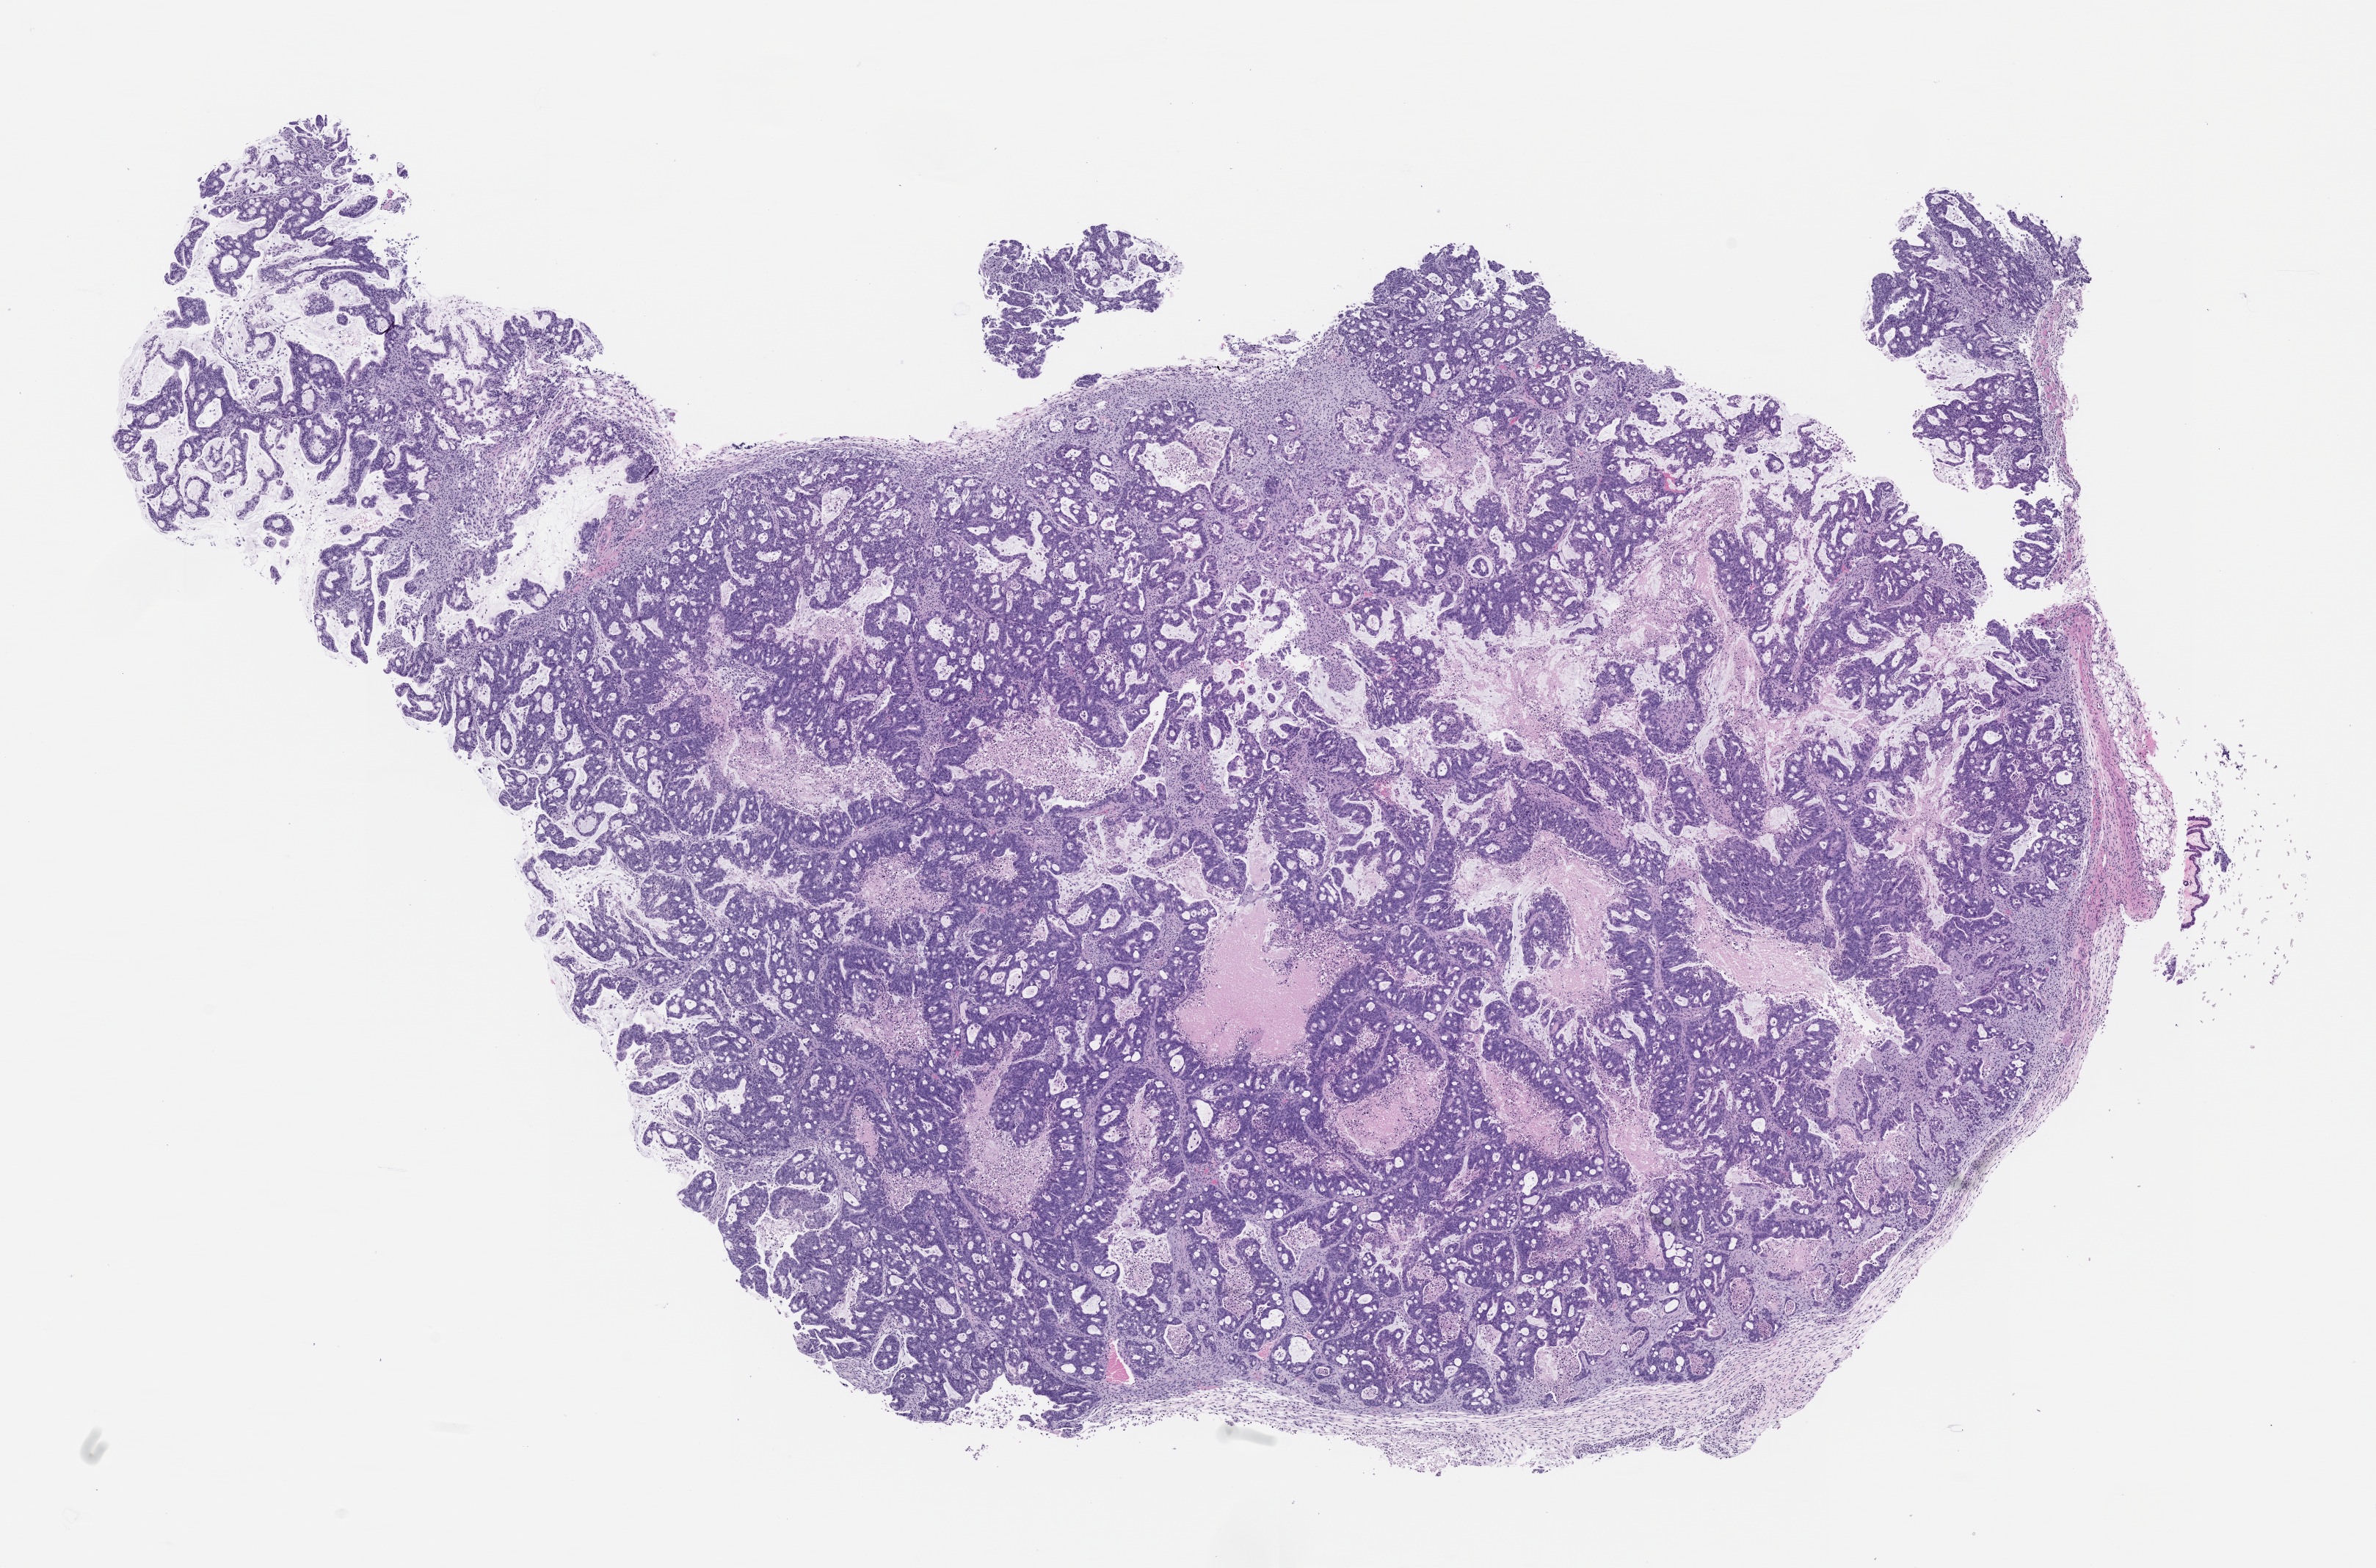
H&E whole-slide image of a patient-derived xenograft (PDX) tumor grown in a mouse, passage 1 — whole scanned area (about 13.0 x 8.6 mm) shown as a low-resolution overview; formalin-fixed, paraffin-embedded (FFPE) tissue; tumor site category: colon.
Originating patient diagnosis: Colon Adenocarcinoma.